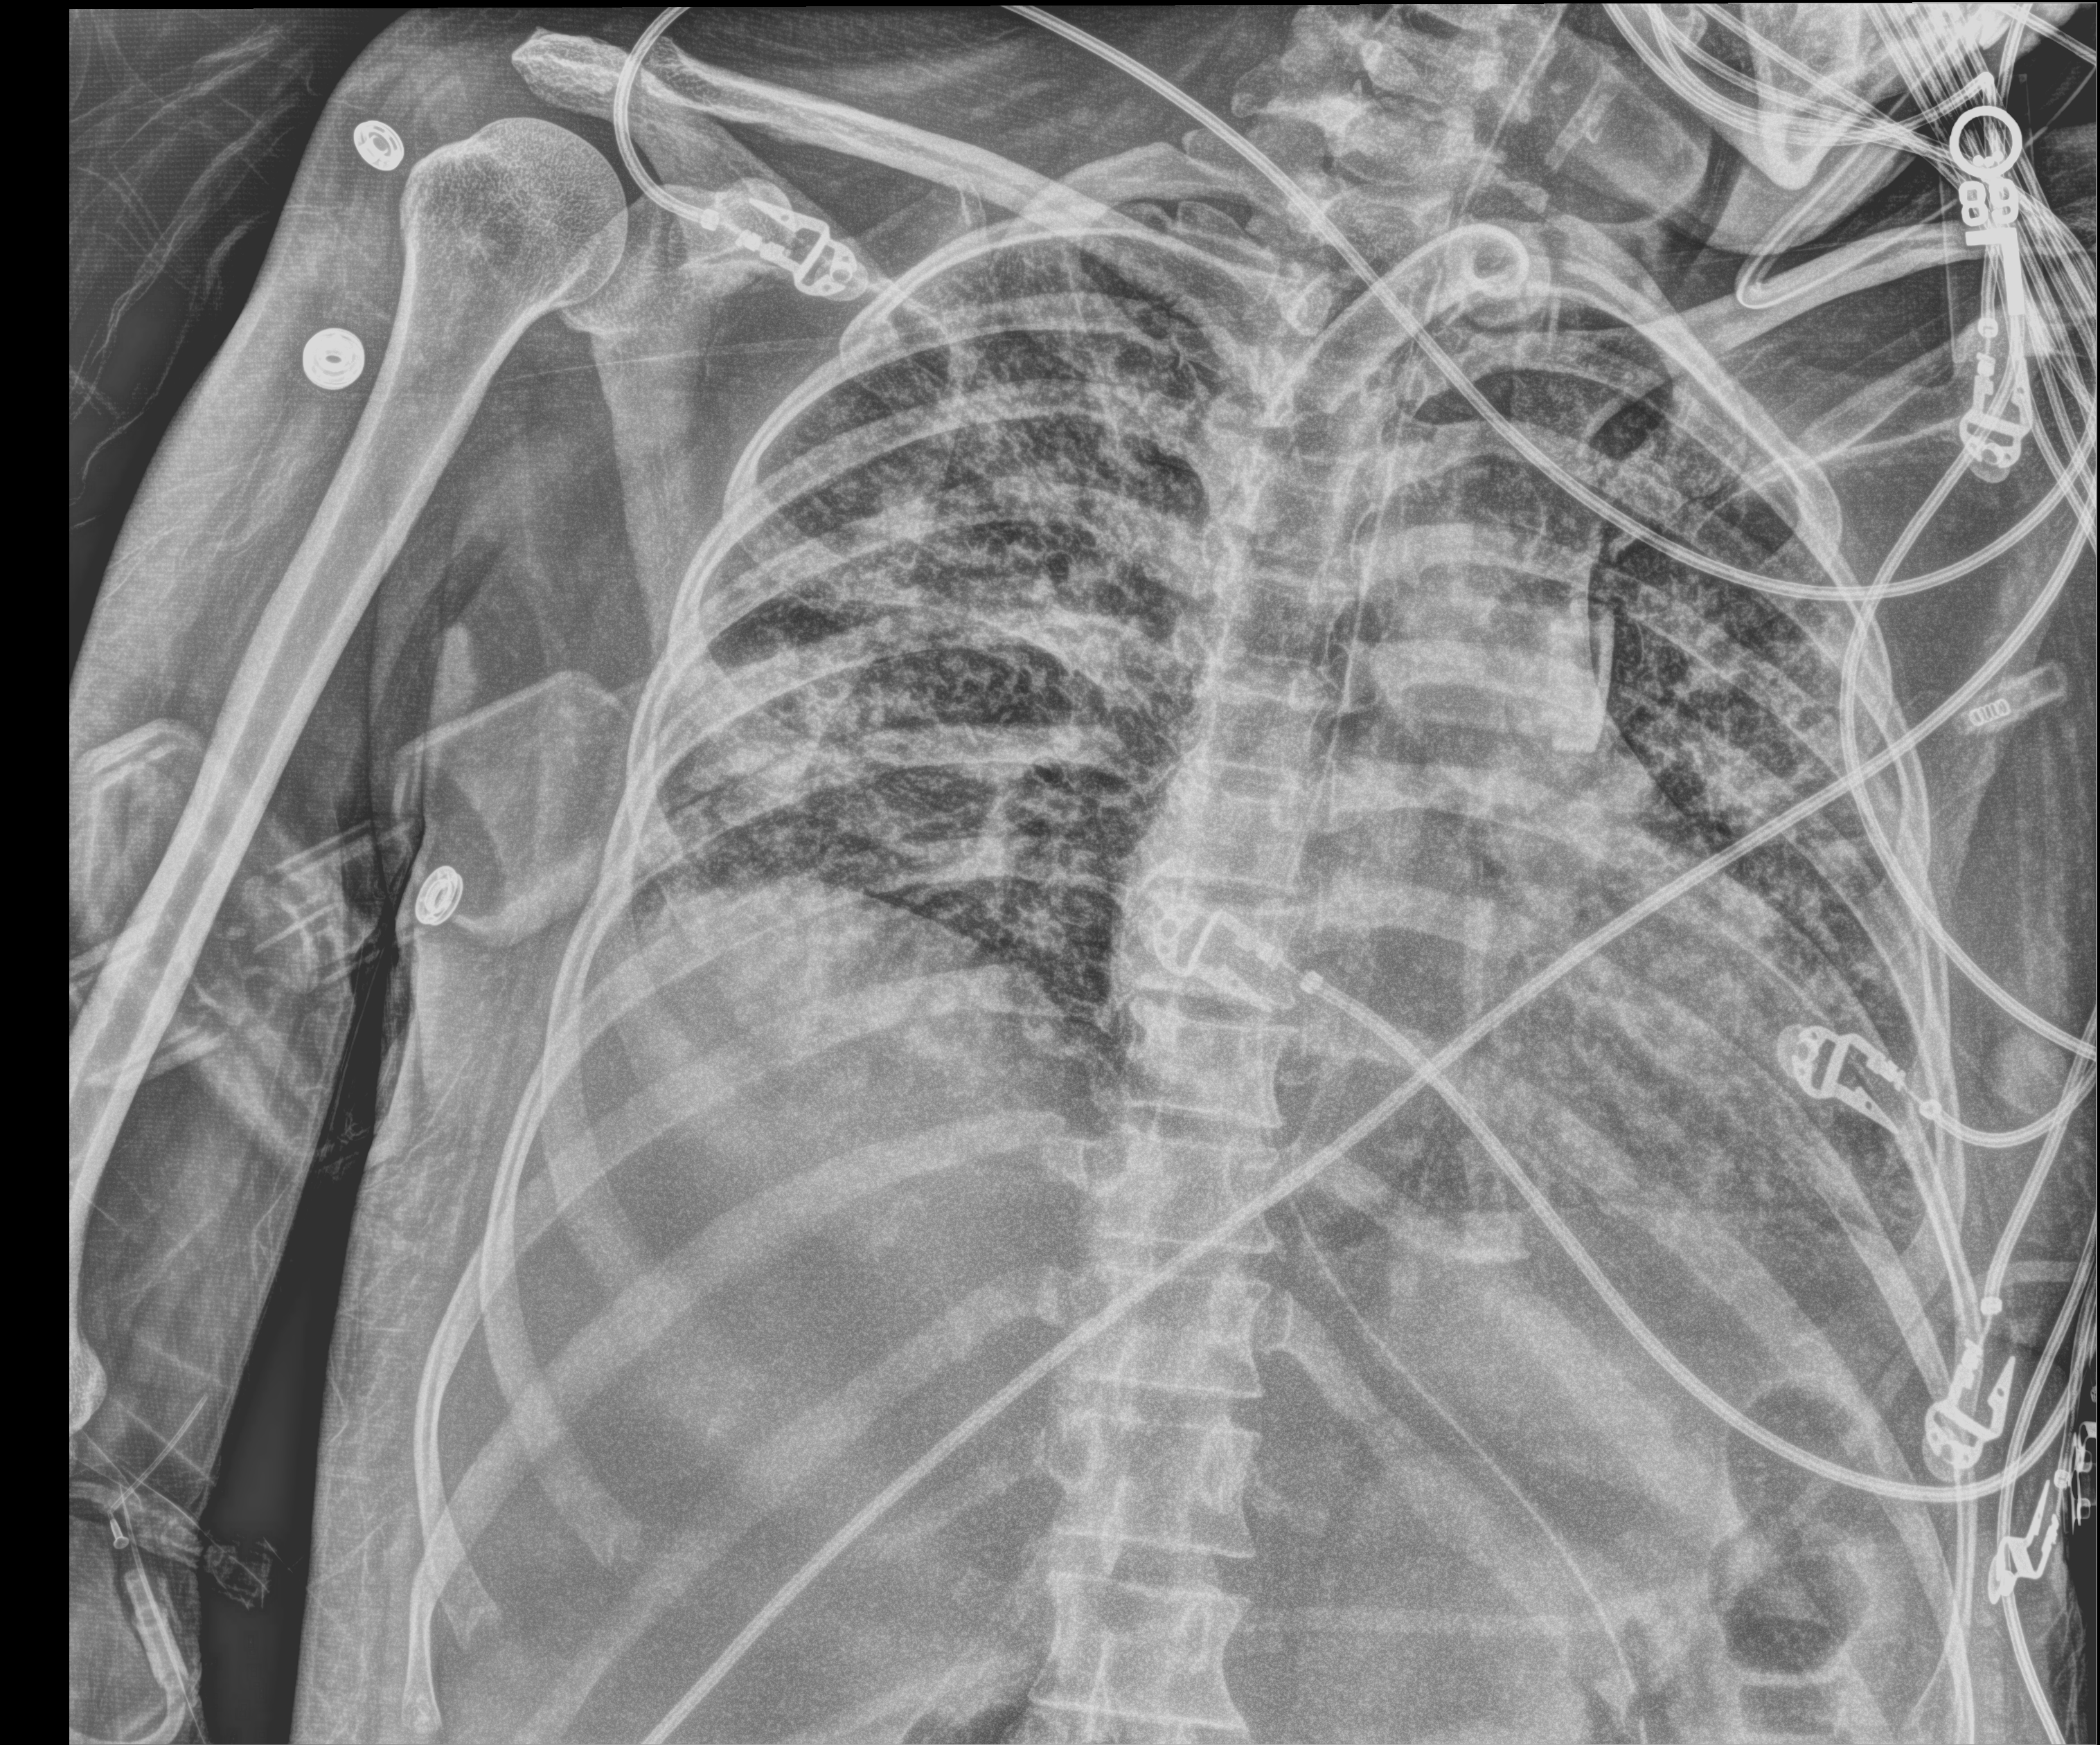
Bedside chest radiograph (digital radiography), anteroposterior (AP) projection. Patient hospitalised with COVID-19; female, aged 18–59 years.
Admission-level facts for this patient (not findings on this image; timing relative to this image not recorded): COPD (admission record): no.